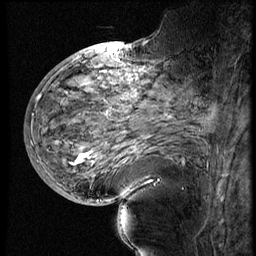
Breast MRI (dynamic contrast-enhanced), one sagittal slice. Position 30 of 60 along the scan axis. 4 images stored at this slice position (order not interpretable as contrast timing). 1.5 T. TE 4.2 ms, TR 9 ms. 2.5 mm slice thickness. 256 × 256 image matrix, field of view 180 × 180 mm. Patient: female, 56 years. From the clinical record (not read from this slice): setting: breast cancer imaged before/during neoadjuvant chemotherapy; receptor status: HER2-positive.
Structures marked on this image (semi-automatic segmentation, software-assisted and operator-edited):
- analysis volume of interest (the breast-tissue region the enhancement analysis was run in; not a lesion): bounding box <82,83,199,177> (left, top, right, bottom; pixels)
- tumour enhancement mask (voxels above the 140 % enhancement threshold inside the analysis volume of interest): <134,147,136,152>